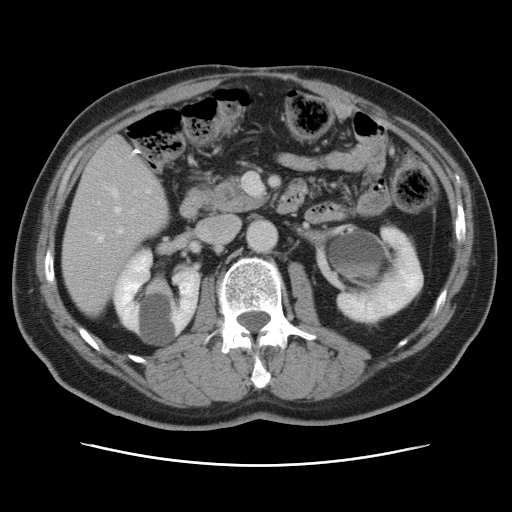
Contrast-enhanced abdominal CT, one axial slice; position 31 of 80 along the scan axis; 120 kVp; intravenous contrast given; soft-tissue window (W 400 / L 40 HU); 5 mm slice thickness; 512 × 512 image matrix, field of view 370 × 370 mm. Male patient, age 69 years. From the clinical record (not read from this slice): diagnosis: colorectal cancer liver metastases, imaged before liver resection; multiple liver metastases: no; largest metastasis: 5 cm; chemotherapy before resection: no.
Annotated regions visible in this slice (outlined manually by an expert reader):
- hepatic veins: bounding box [x1, y1, x2, y2] px = [93, 188, 120, 242]
- liver: [63, 137, 168, 314]
- planned liver remnant (the part of the liver to remain after resection): [63, 213, 146, 314]
- portal vein (with intrahepatic branches): [102, 228, 123, 277]